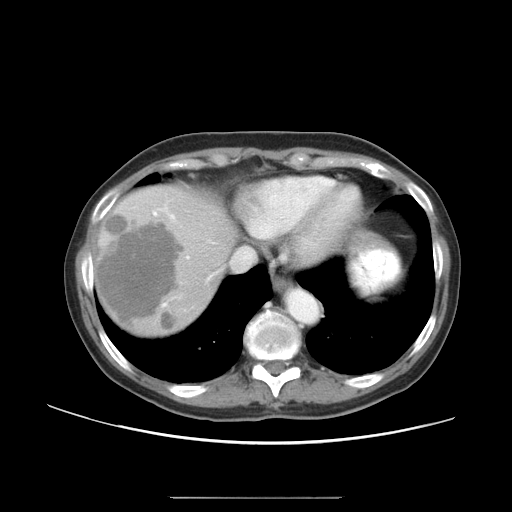
Contrast-enhanced abdominal CT, one axial slice. Slice 41 of 50 in the series (ordered by position). Intravenous contrast given. Soft-tissue window (W 400 / L 40 HU). 5 mm slice thickness. 512 × 512 image matrix. Female patient, age 58 years. From the clinical record (not read from this slice): diagnosis: colorectal cancer liver metastases, imaged before liver resection; multiple liver metastases: yes; largest metastasis: 7.3 cm; disease in both lobes: yes.
Structures marked on this image (manually delineated by an expert):
- hepatic veins: bounding box (x1, y1, x2, y2) in pixels: (170, 214, 254, 271)
- liver: (96, 185, 232, 335)
- planned liver remnant (the part of the liver to remain after resection): (198, 197, 232, 242)
- portal vein (with intrahepatic branches): (153, 209, 160, 216)
- liver metastasis: (161, 317, 175, 330)
- liver metastasis: (98, 214, 183, 329)